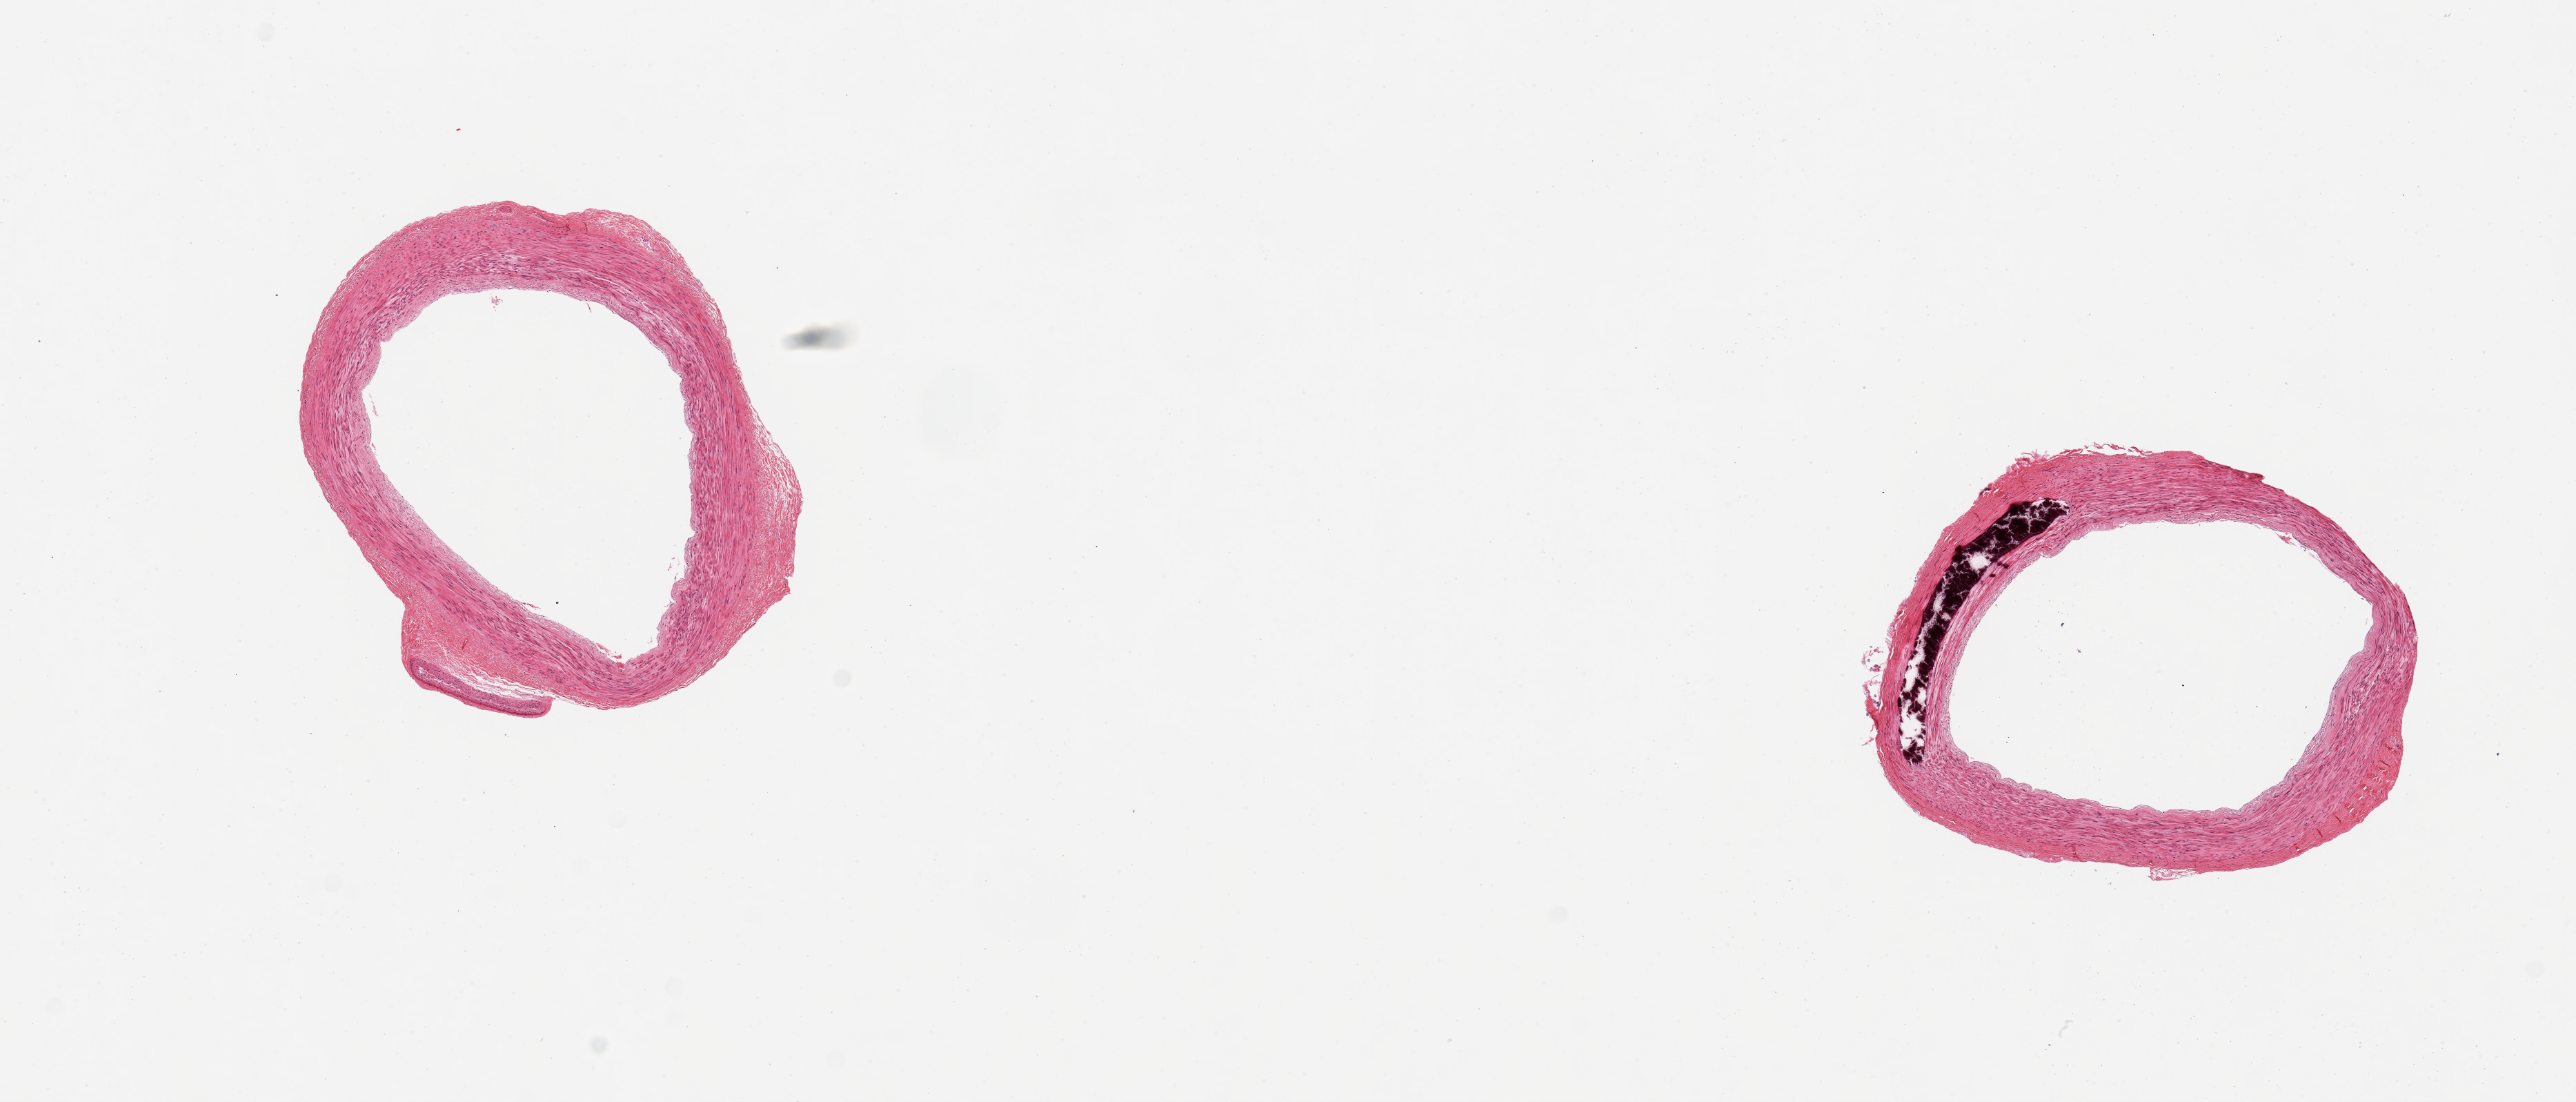
Digitized hematoxylin and eosin (H&E)-stained section — shown as a low-resolution overview of the whole scanned area (about 14.8 x 6.3 mm), PAXgene-fixed paraffin-embedded (PFPE) section, sampled site (target tissue): tibial artery, tissue donor sample. Donor: male.
Pathologist's review note for this sample: 2 pieces; well trimmed with medial calcification in one section.